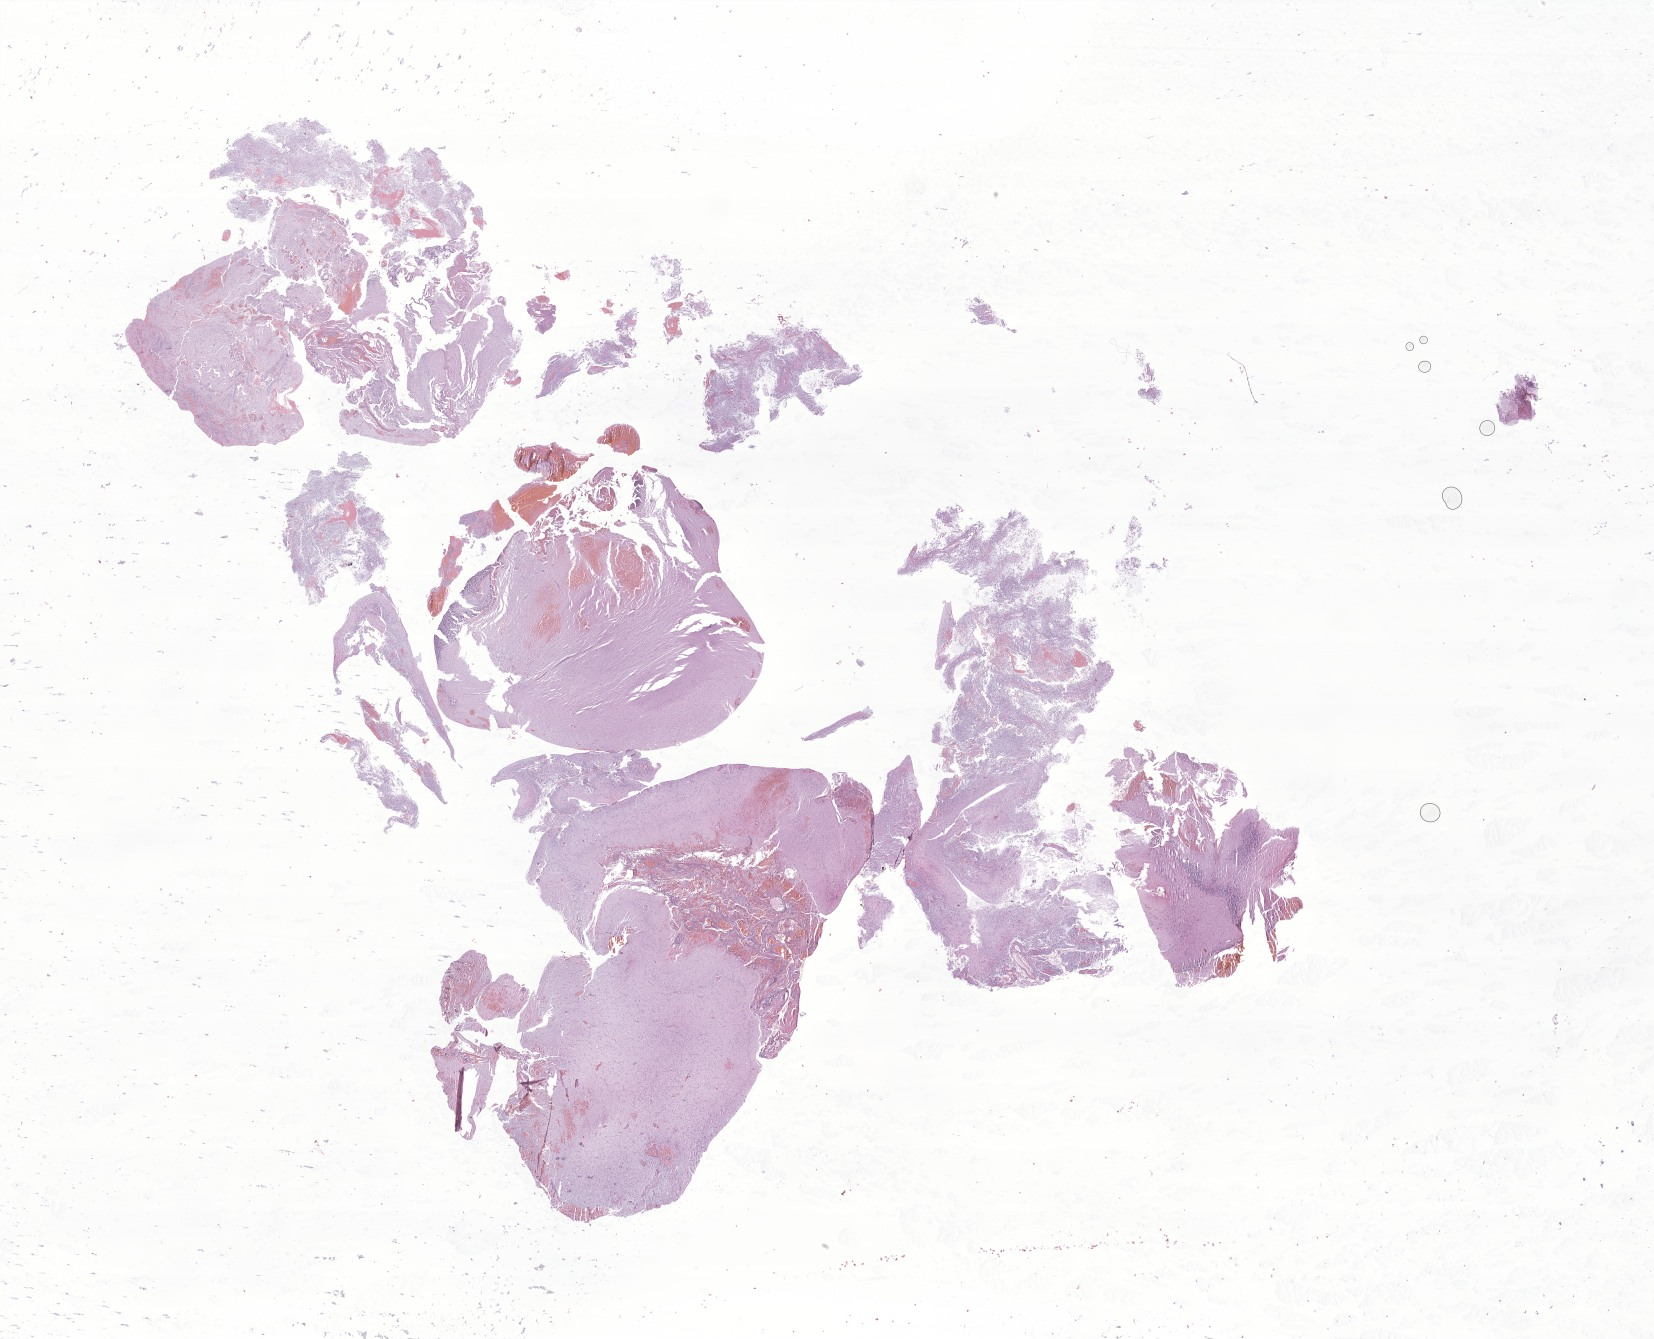
Hematoxylin and eosin (H&E) whole-slide image of tumor tissue from the brain stem — whole scanned area (about 27.9 x 22.6 mm) shown as a low-resolution overview; FFPE section. Patient female; age 57 months (4 years 9 months).
Diagnosis (ICD-O-3 morphology term): Astrocytoma, NOS.